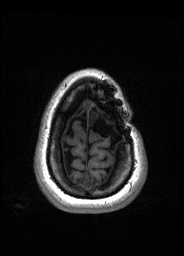
Pre-operative brain MRI before brain-tumour surgery, one axial slice; slice 32 of 176 in the series (ordered by position); T1-weighted post-contrast; 184 × 256 image matrix, field of view 180 × 250 mm. From the clinical record (not read from this slice): histopathology: Oligodendroglioma; WHO grade: 2; IDH mutation: yes.
Outlined on this slice (manually delineated by an expert):
- tumour: box from (x=88, y=110) to (x=99, y=126) px